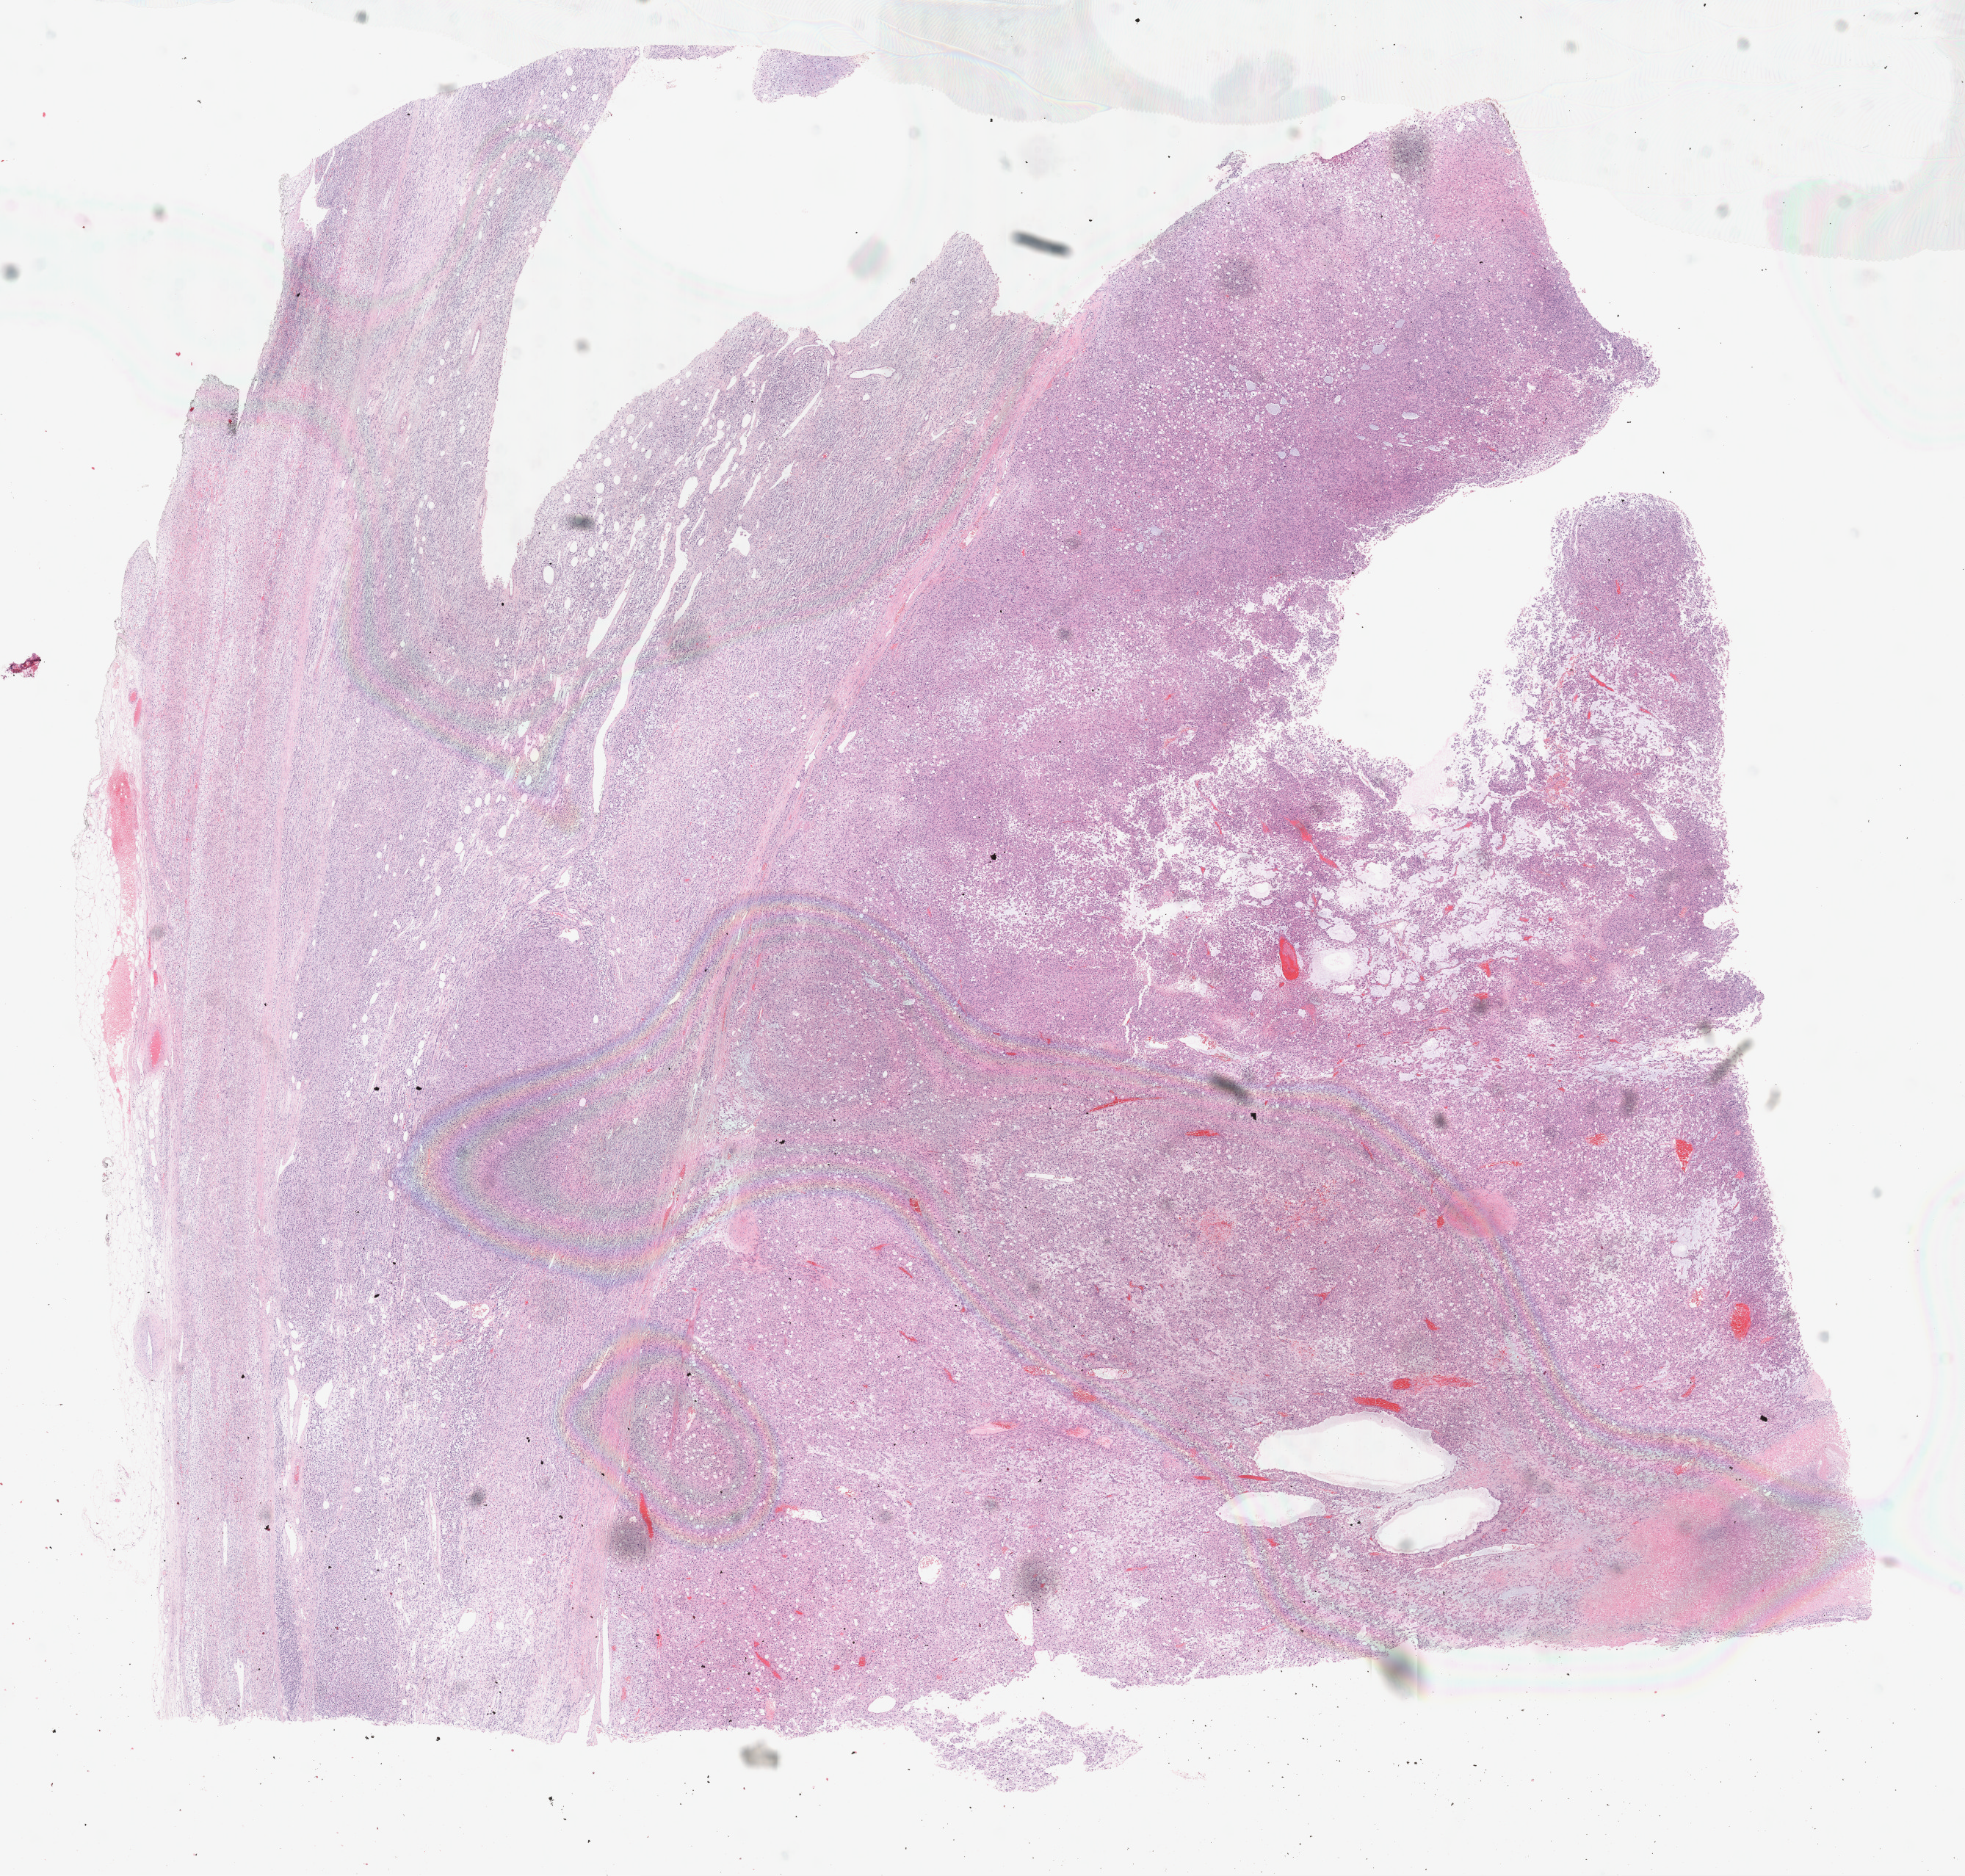
Whole-slide histology image, Hematoxylin and eosin (H&E) stained — whole scanned area (about 21.6 x 20.7 mm, from a 40x scan) shown as a low-resolution overview; FFPE section; primary tumour sample from the adrenal cortex. Male patient; age at initial diagnosis 40 years.
Pathologic diagnosis: Adrenal cortical carcinoma (cortex of adrenal gland).